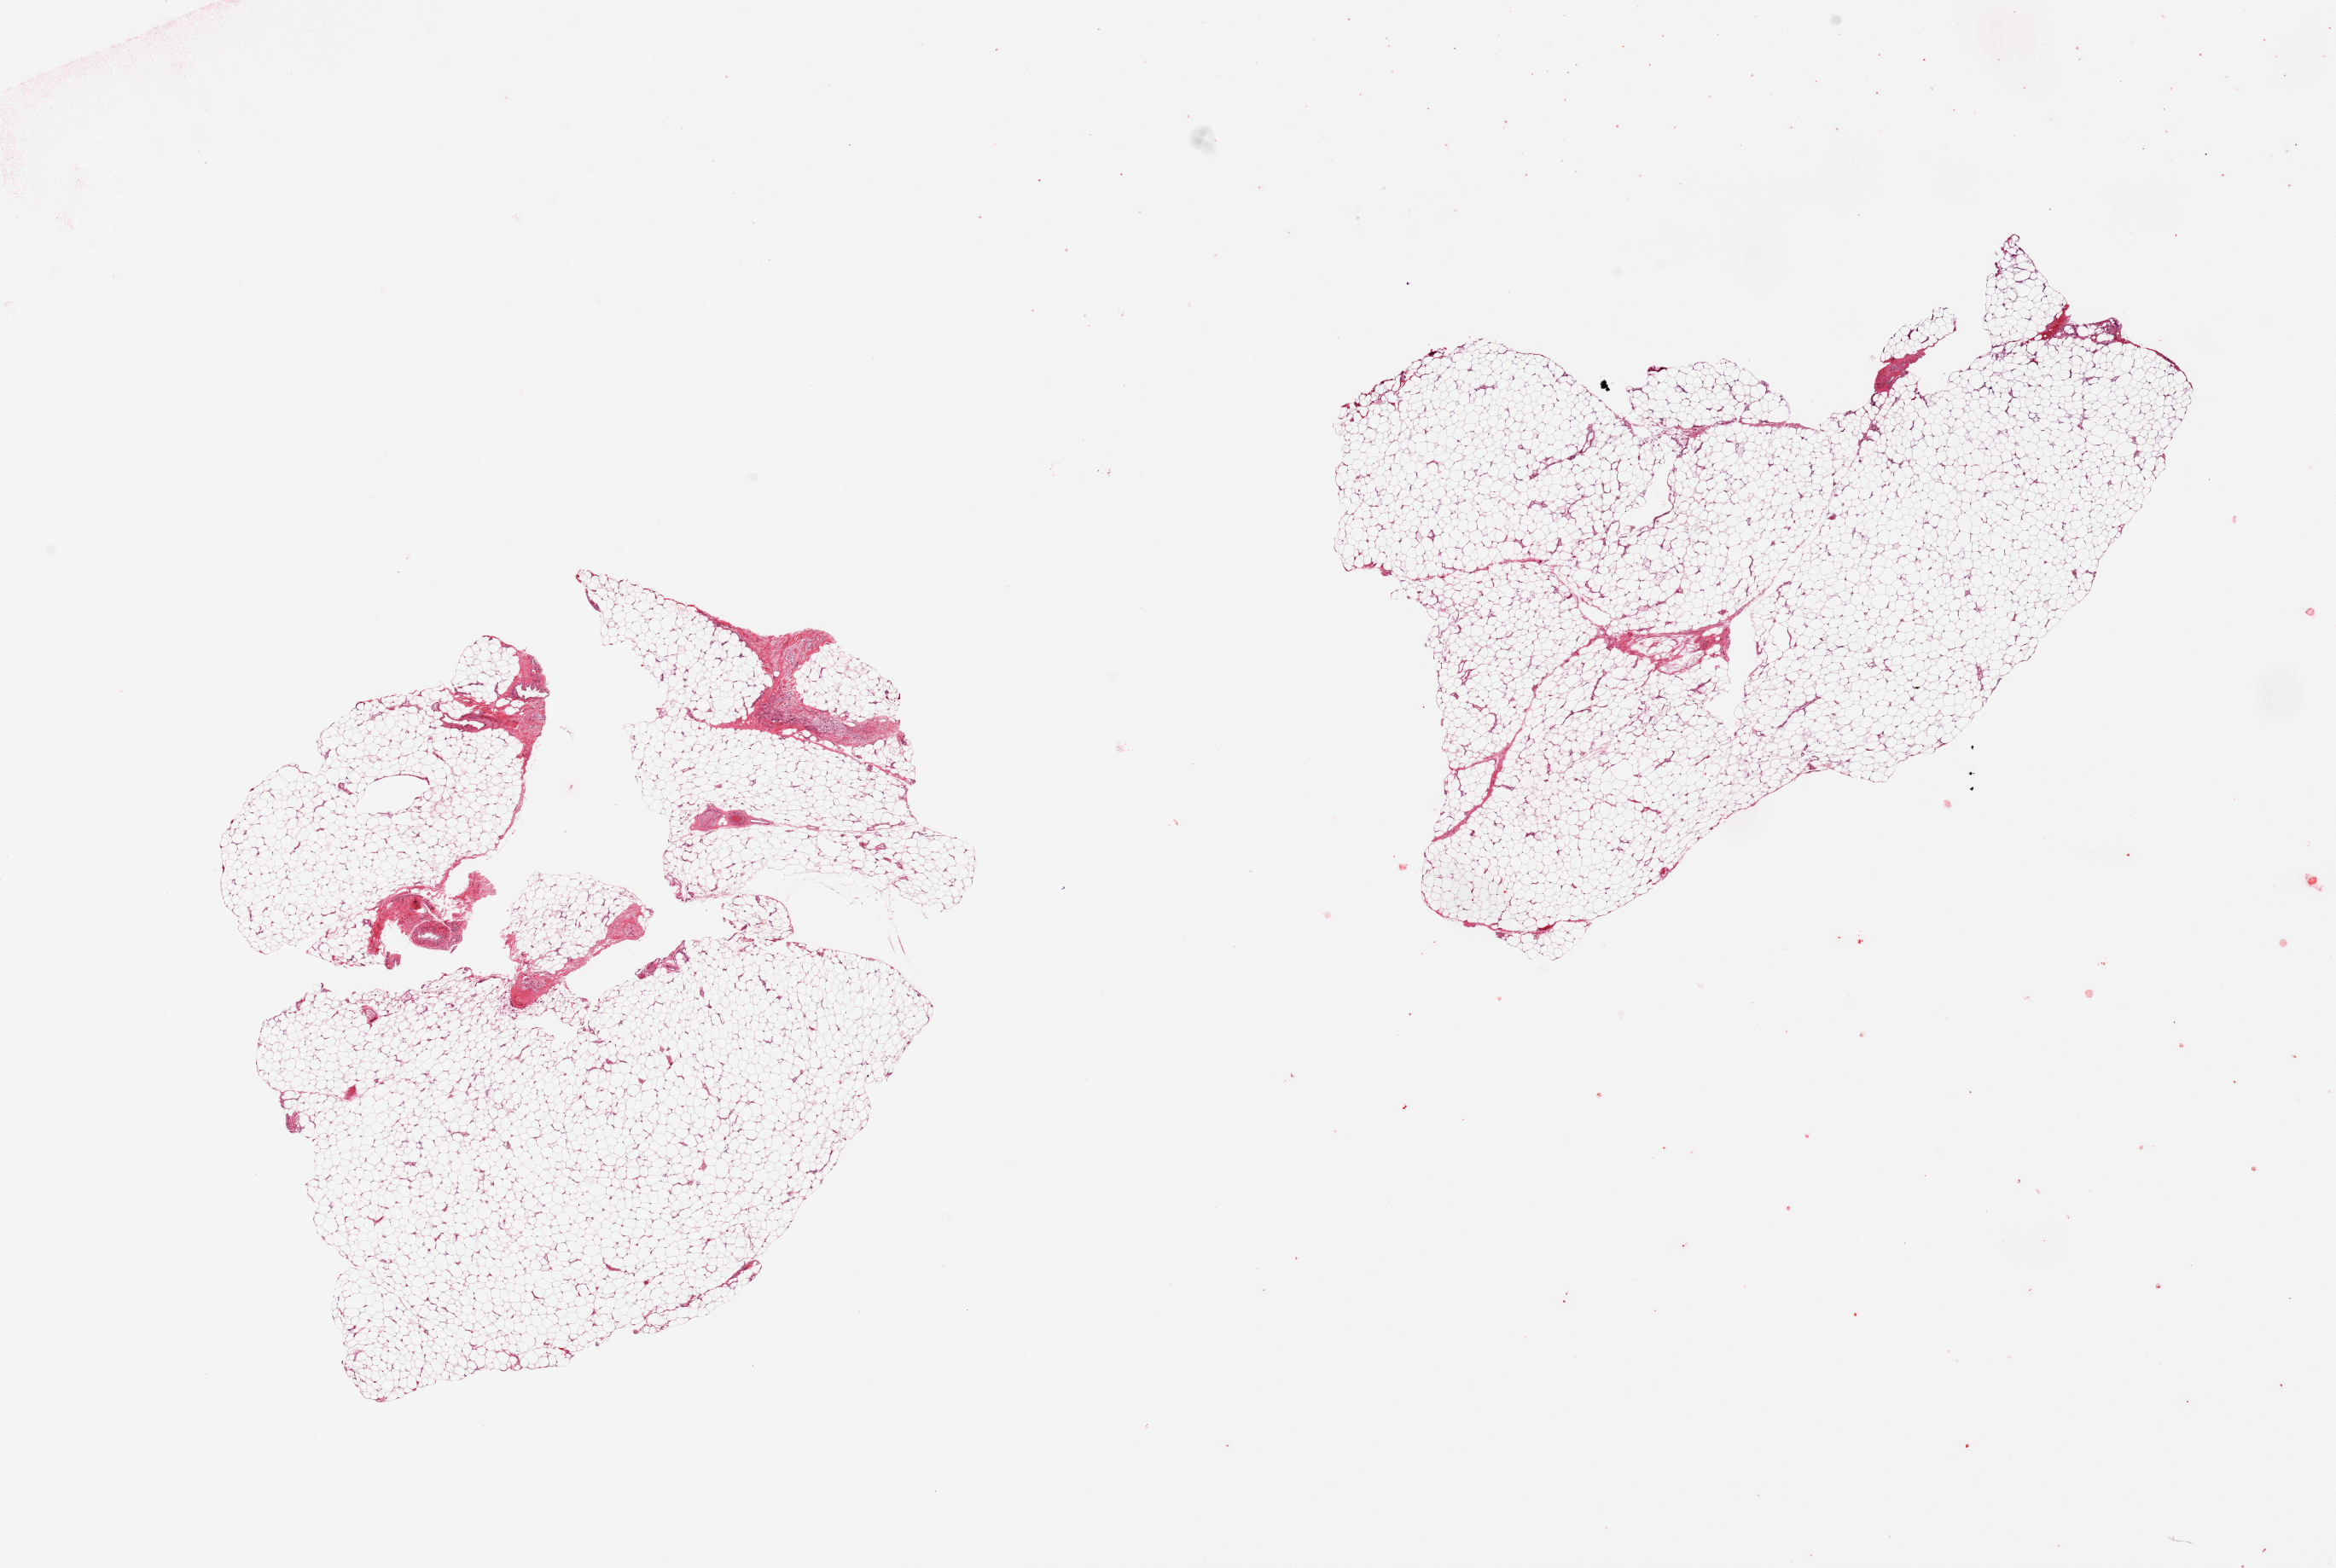
Haematoxylin and eosin whole-slide image, a low-resolution overview of the entire scanned area, about 21.7 x 14.5 mm (from a 20x scan), PAXgene-fixed paraffin-embedded (PFPE) section, sampled site (target tissue): adipose tissue, donor tissue sample. Female donor.
Review note (as recorded): 2 pieces; <5% fibrous content.